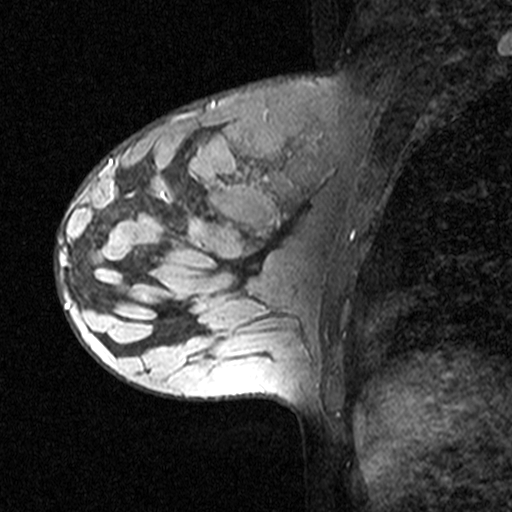
Breast MRI (dynamic contrast-enhanced), one sagittal slice. Dynamic contrast-enhanced study with each time point stored as its own series, time point 2 of 3 at this slice position (early post-contrast, ordered by acquisition time). 1.5 T. TE 4.5 ms, TR 11 ms. 3 mm slice thickness. 512 × 512 image matrix. Female patient, age 27 years. Case-level facts recorded for this patient, not image findings: setting: breast cancer imaged before/during neoadjuvant chemotherapy; receptor status: HR-positive, HER2-negative.
Structures marked on this image (semi-automatically segmented with operator editing):
- analysis volume of interest (the breast-tissue region the enhancement analysis was run in; not a lesion): box from (x=56, y=162) to (x=163, y=271) px
- tumour enhancement mask (voxels above the 90 % enhancement threshold inside the analysis volume of interest): (x=58, y=162)–(x=135, y=271)